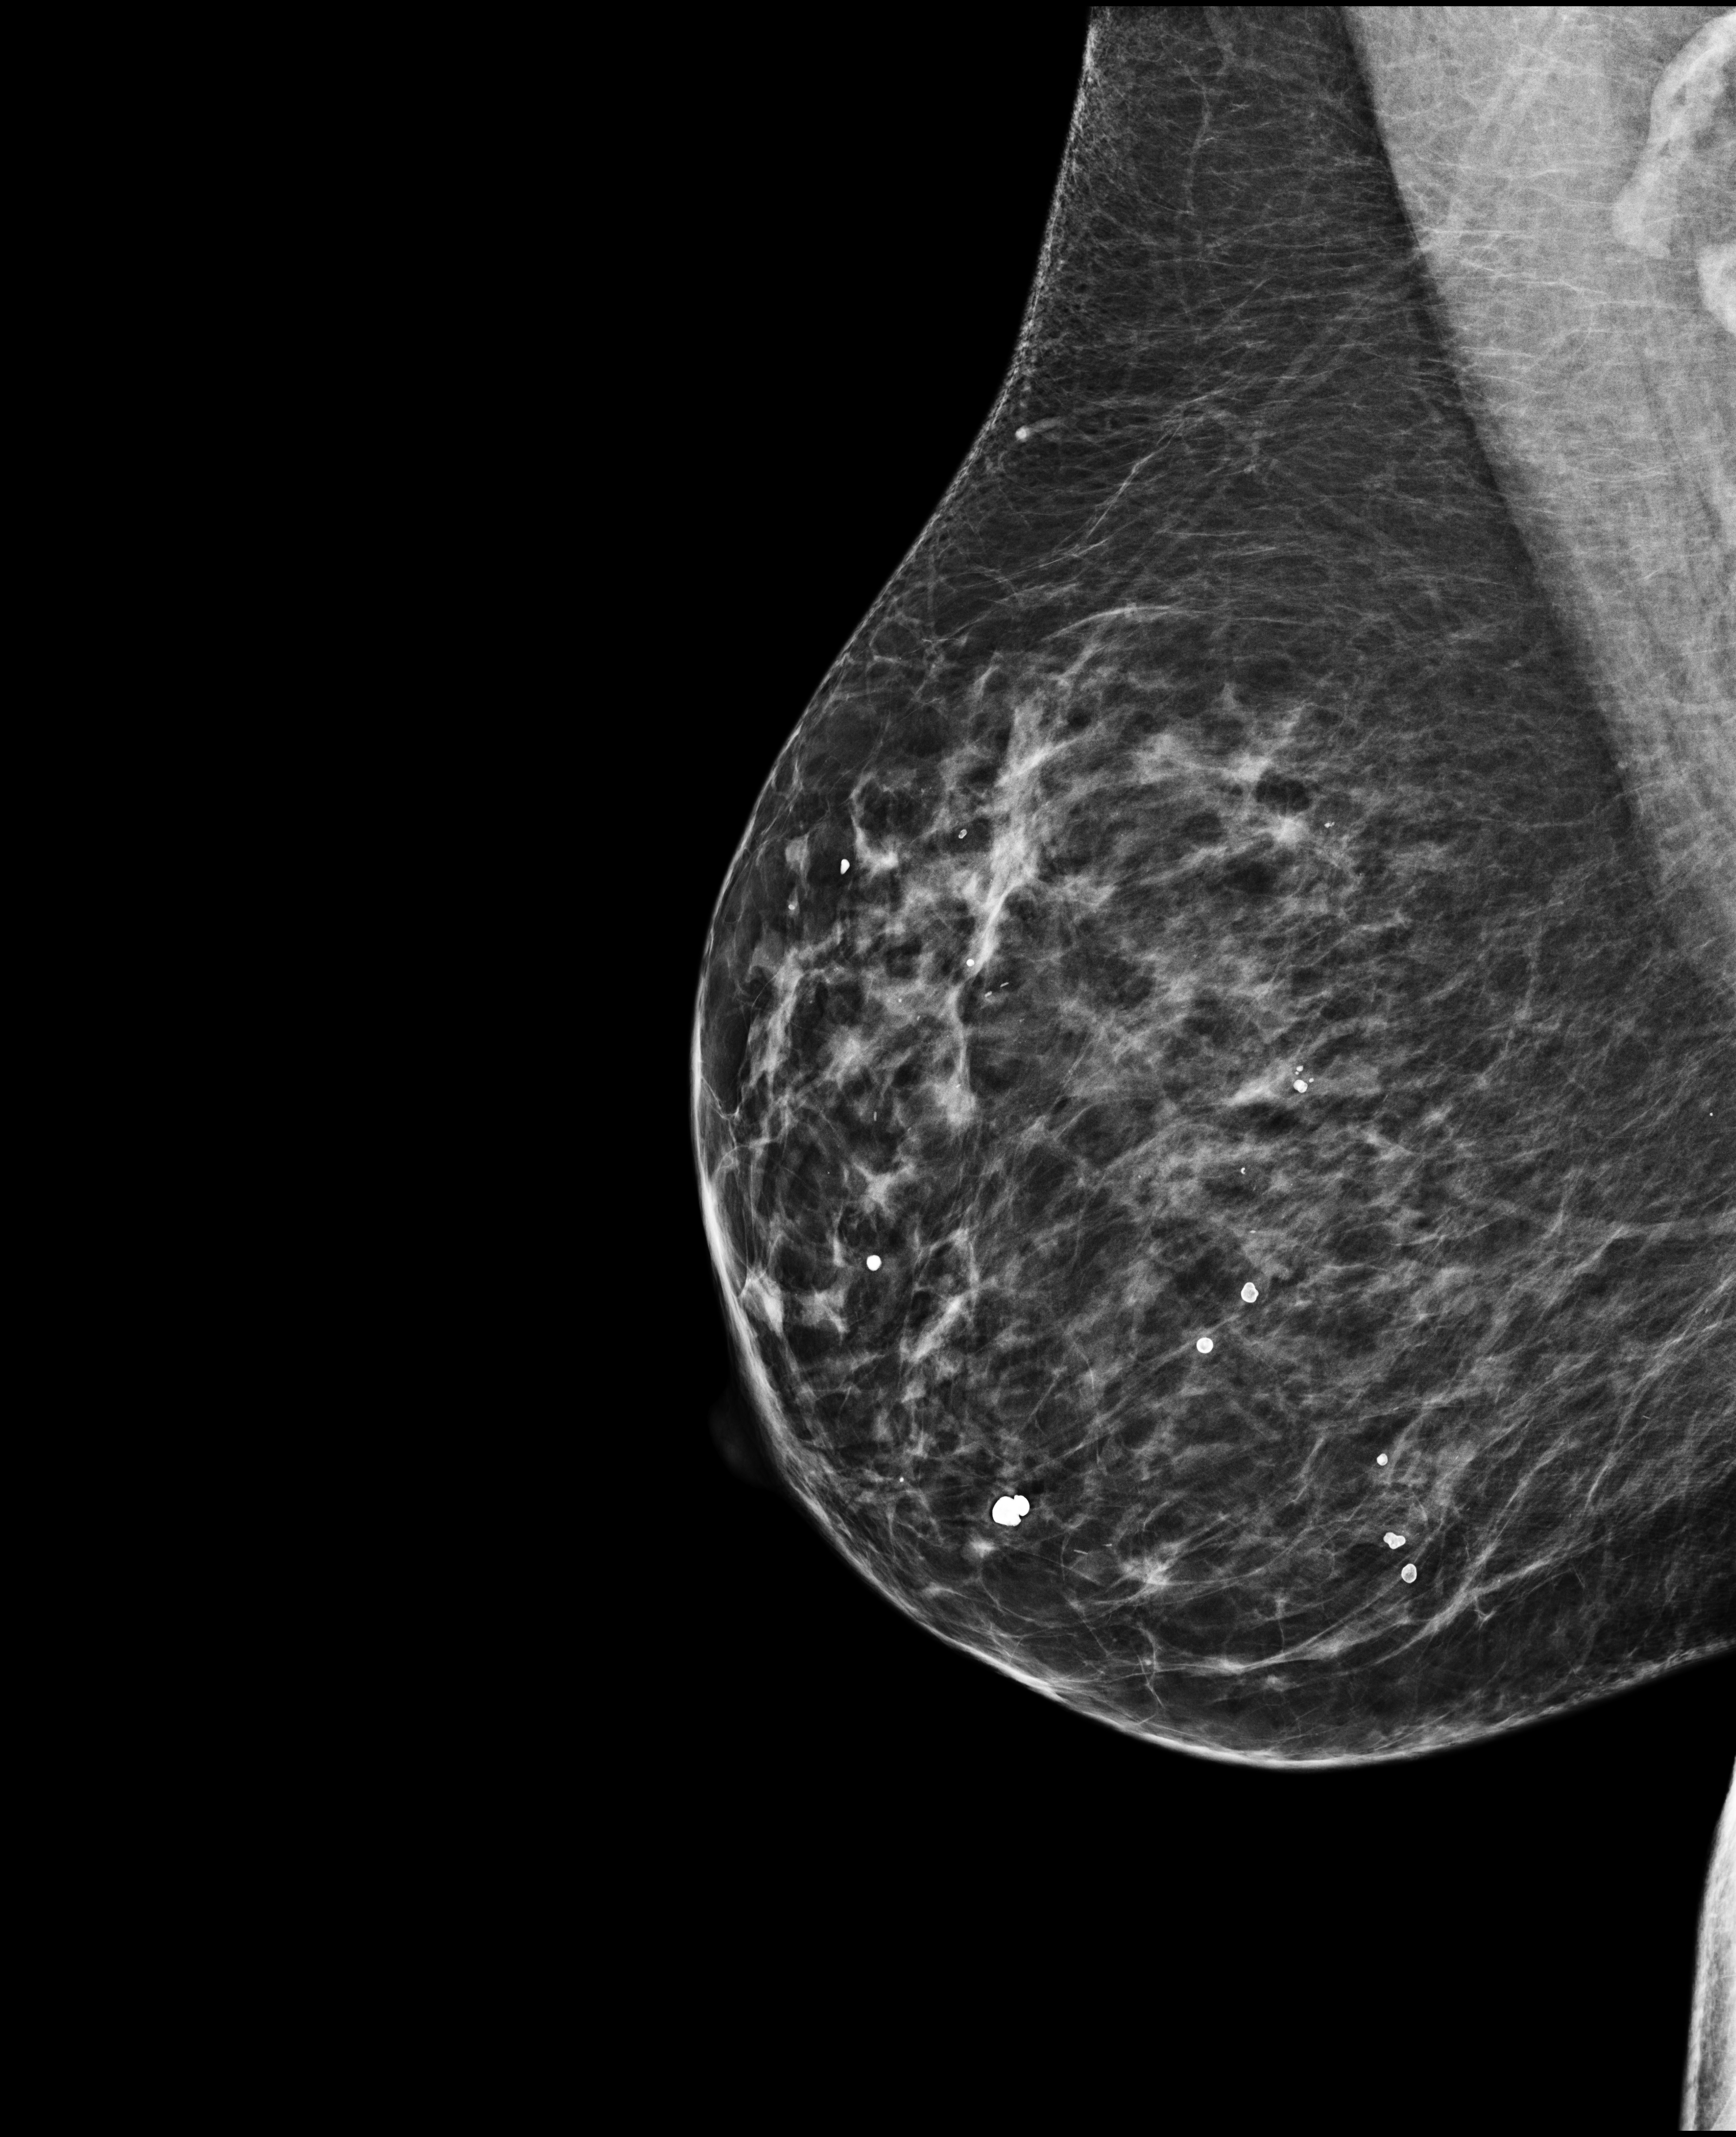
Screening examination. Patient: female, 66 years.
Image type: full-field digital mammogram. Breast: right. Projection: MLO view.